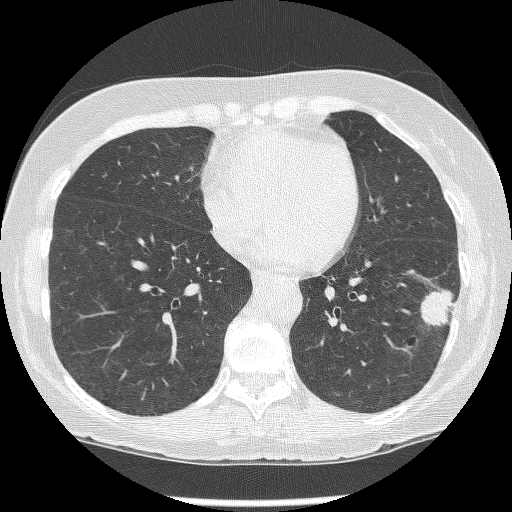
Chest CT (low-dose screening protocol), one axial image. Baseline annual screen. Lung window (W 1500 / L -600 HU). 1.25 mm slice thickness. Lung (sharp) reconstruction kernel (BONE). 120 kVp. Slice 94 of 247 in the series. Female participant, aged 62 years at enrolment. Former smoker at enrolment.
• Lesion marked by an expert reader, bounding box (x1, y1, x2, y2) in pixels: (417, 283, 461, 337).
• The screening reader recorded 2 non-calcified nodules or masses ≥4 mm on this exam (left lower lobe, left lower lobe); which of them this box marks is not recorded.
• Participant outcome: lung cancer diagnosed 15 days after this screen — non-small cell carcinoma, left lower lobe, stage IIIB (AJCC 6th edition), 23 mm at pathology.